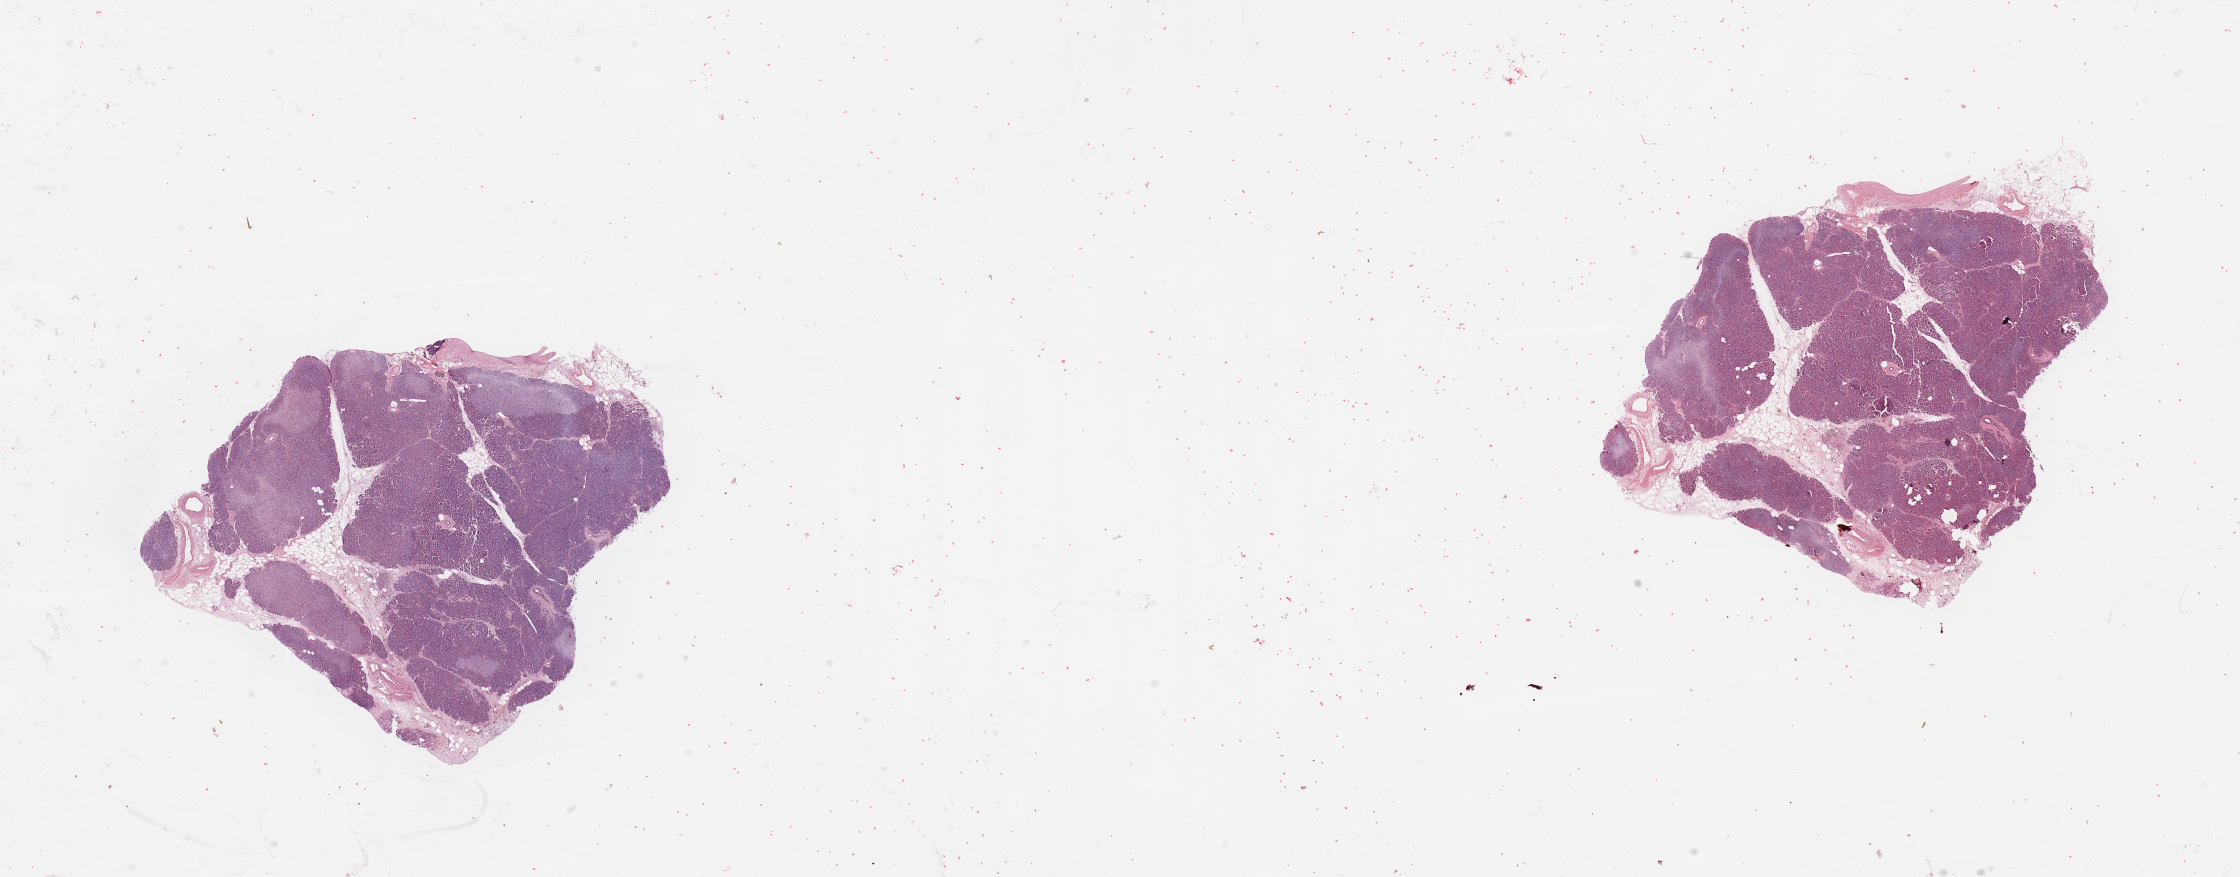
Digitized H&E tissue section (whole slide) — a low-resolution overview of the entire scanned area, about 35.4 x 13.9 mm (slide scanned at 20x), pancreas, tissue type not recorded.
- patient diagnosis (cohort enrolment): ductal adenocarcinoma (pancreas)